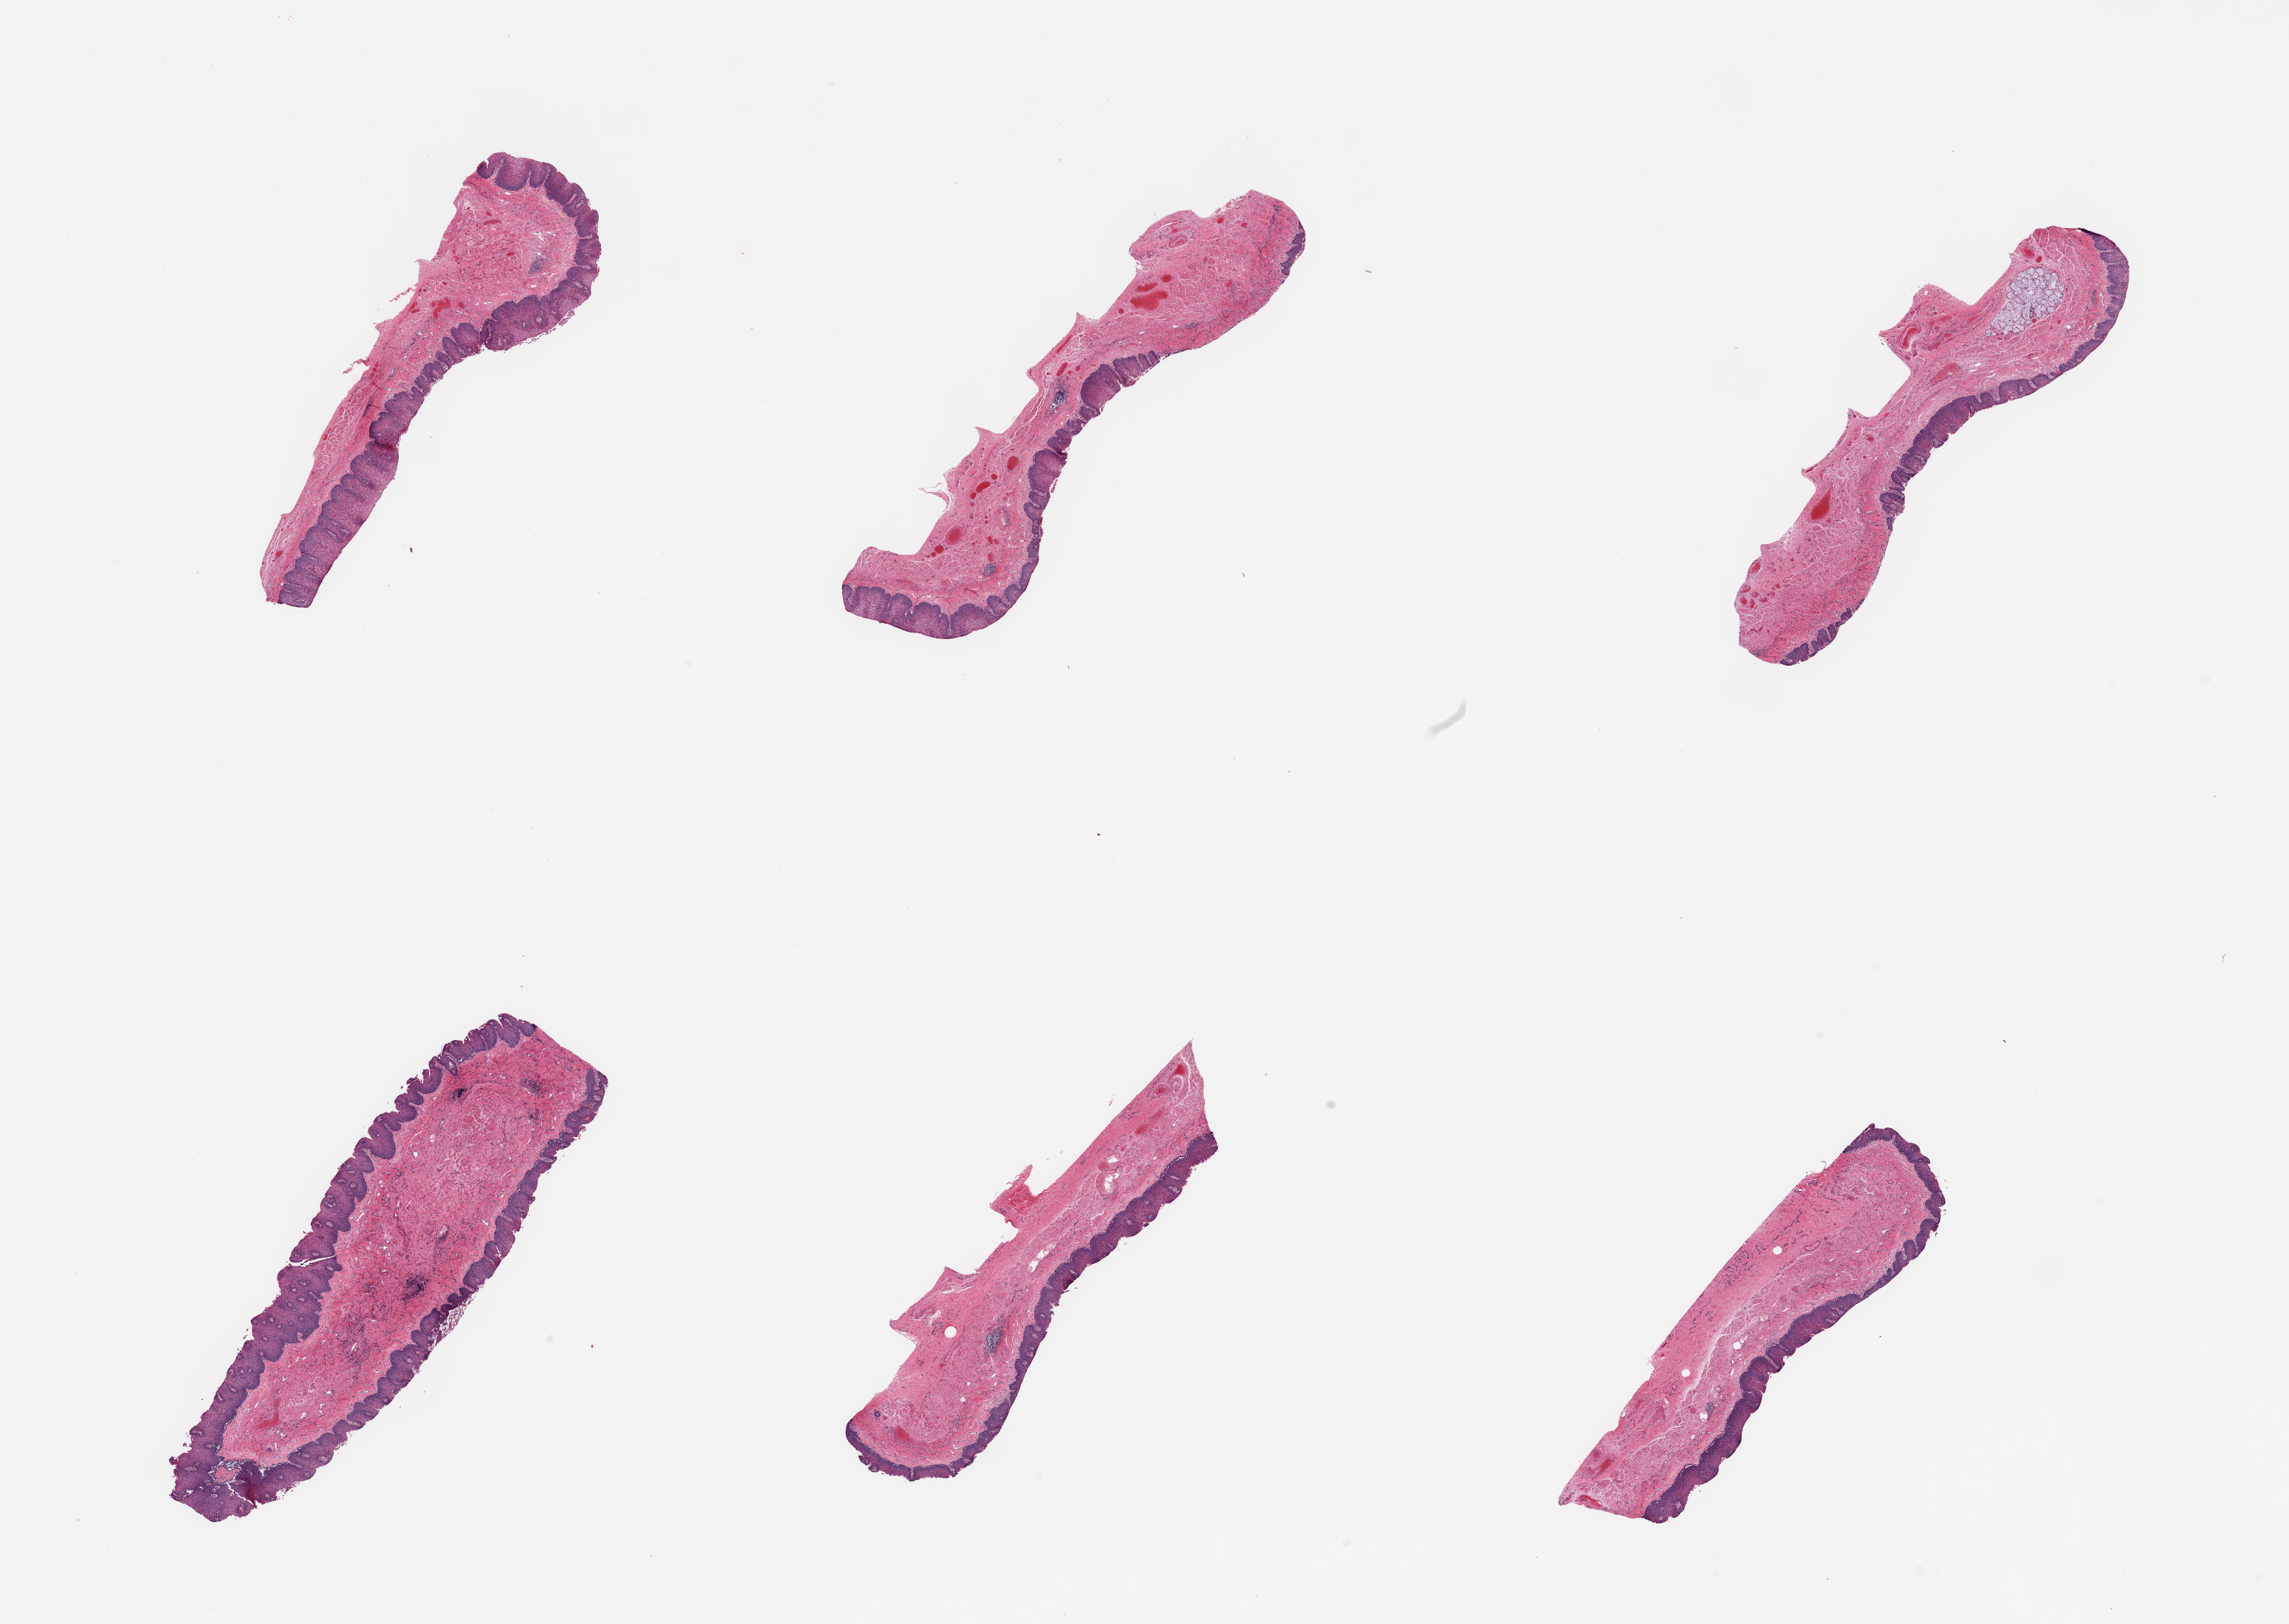
Digitized H&E-stained section — a low-resolution overview of the entire scanned area, about 24.6 x 17.5 mm, PAXgene-fixed paraffin-embedded (PFPE) section, target tissue: esophageal mucous membrane, tissue donor sample.
Reviewer comment on this tissue sample: 6 pieces; includes few clusters of submucosal glands.